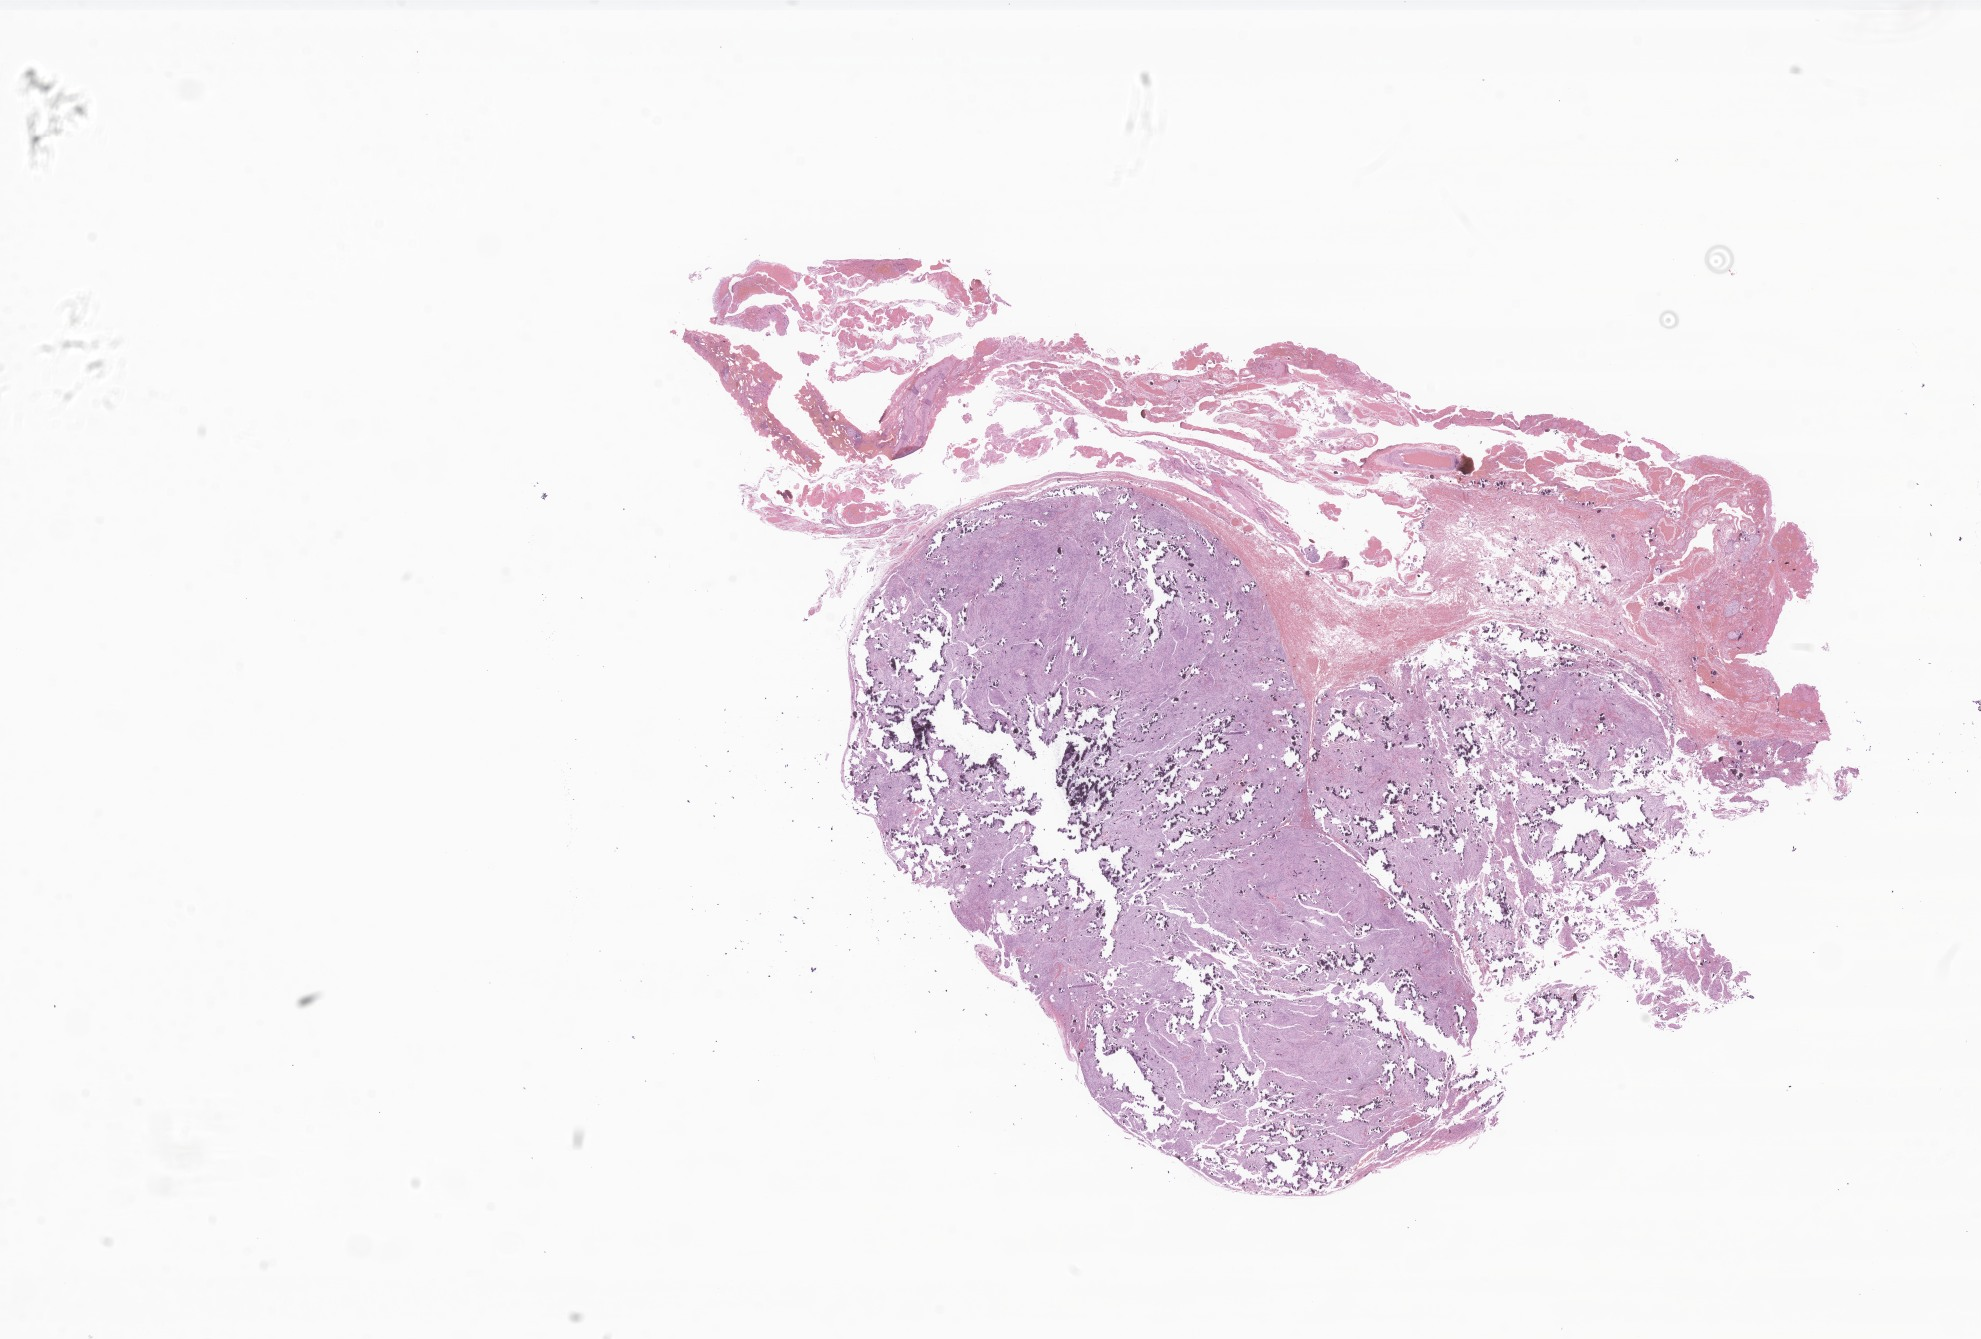
H&E whole-slide image of tumor tissue from the brain, a low-resolution overview of the entire scanned area, about 33.4 x 22.6 mm, FFPE section. Patient: male, age 242 months (20 years 2 months).
Recorded diagnosis: Meningioma, NOS.